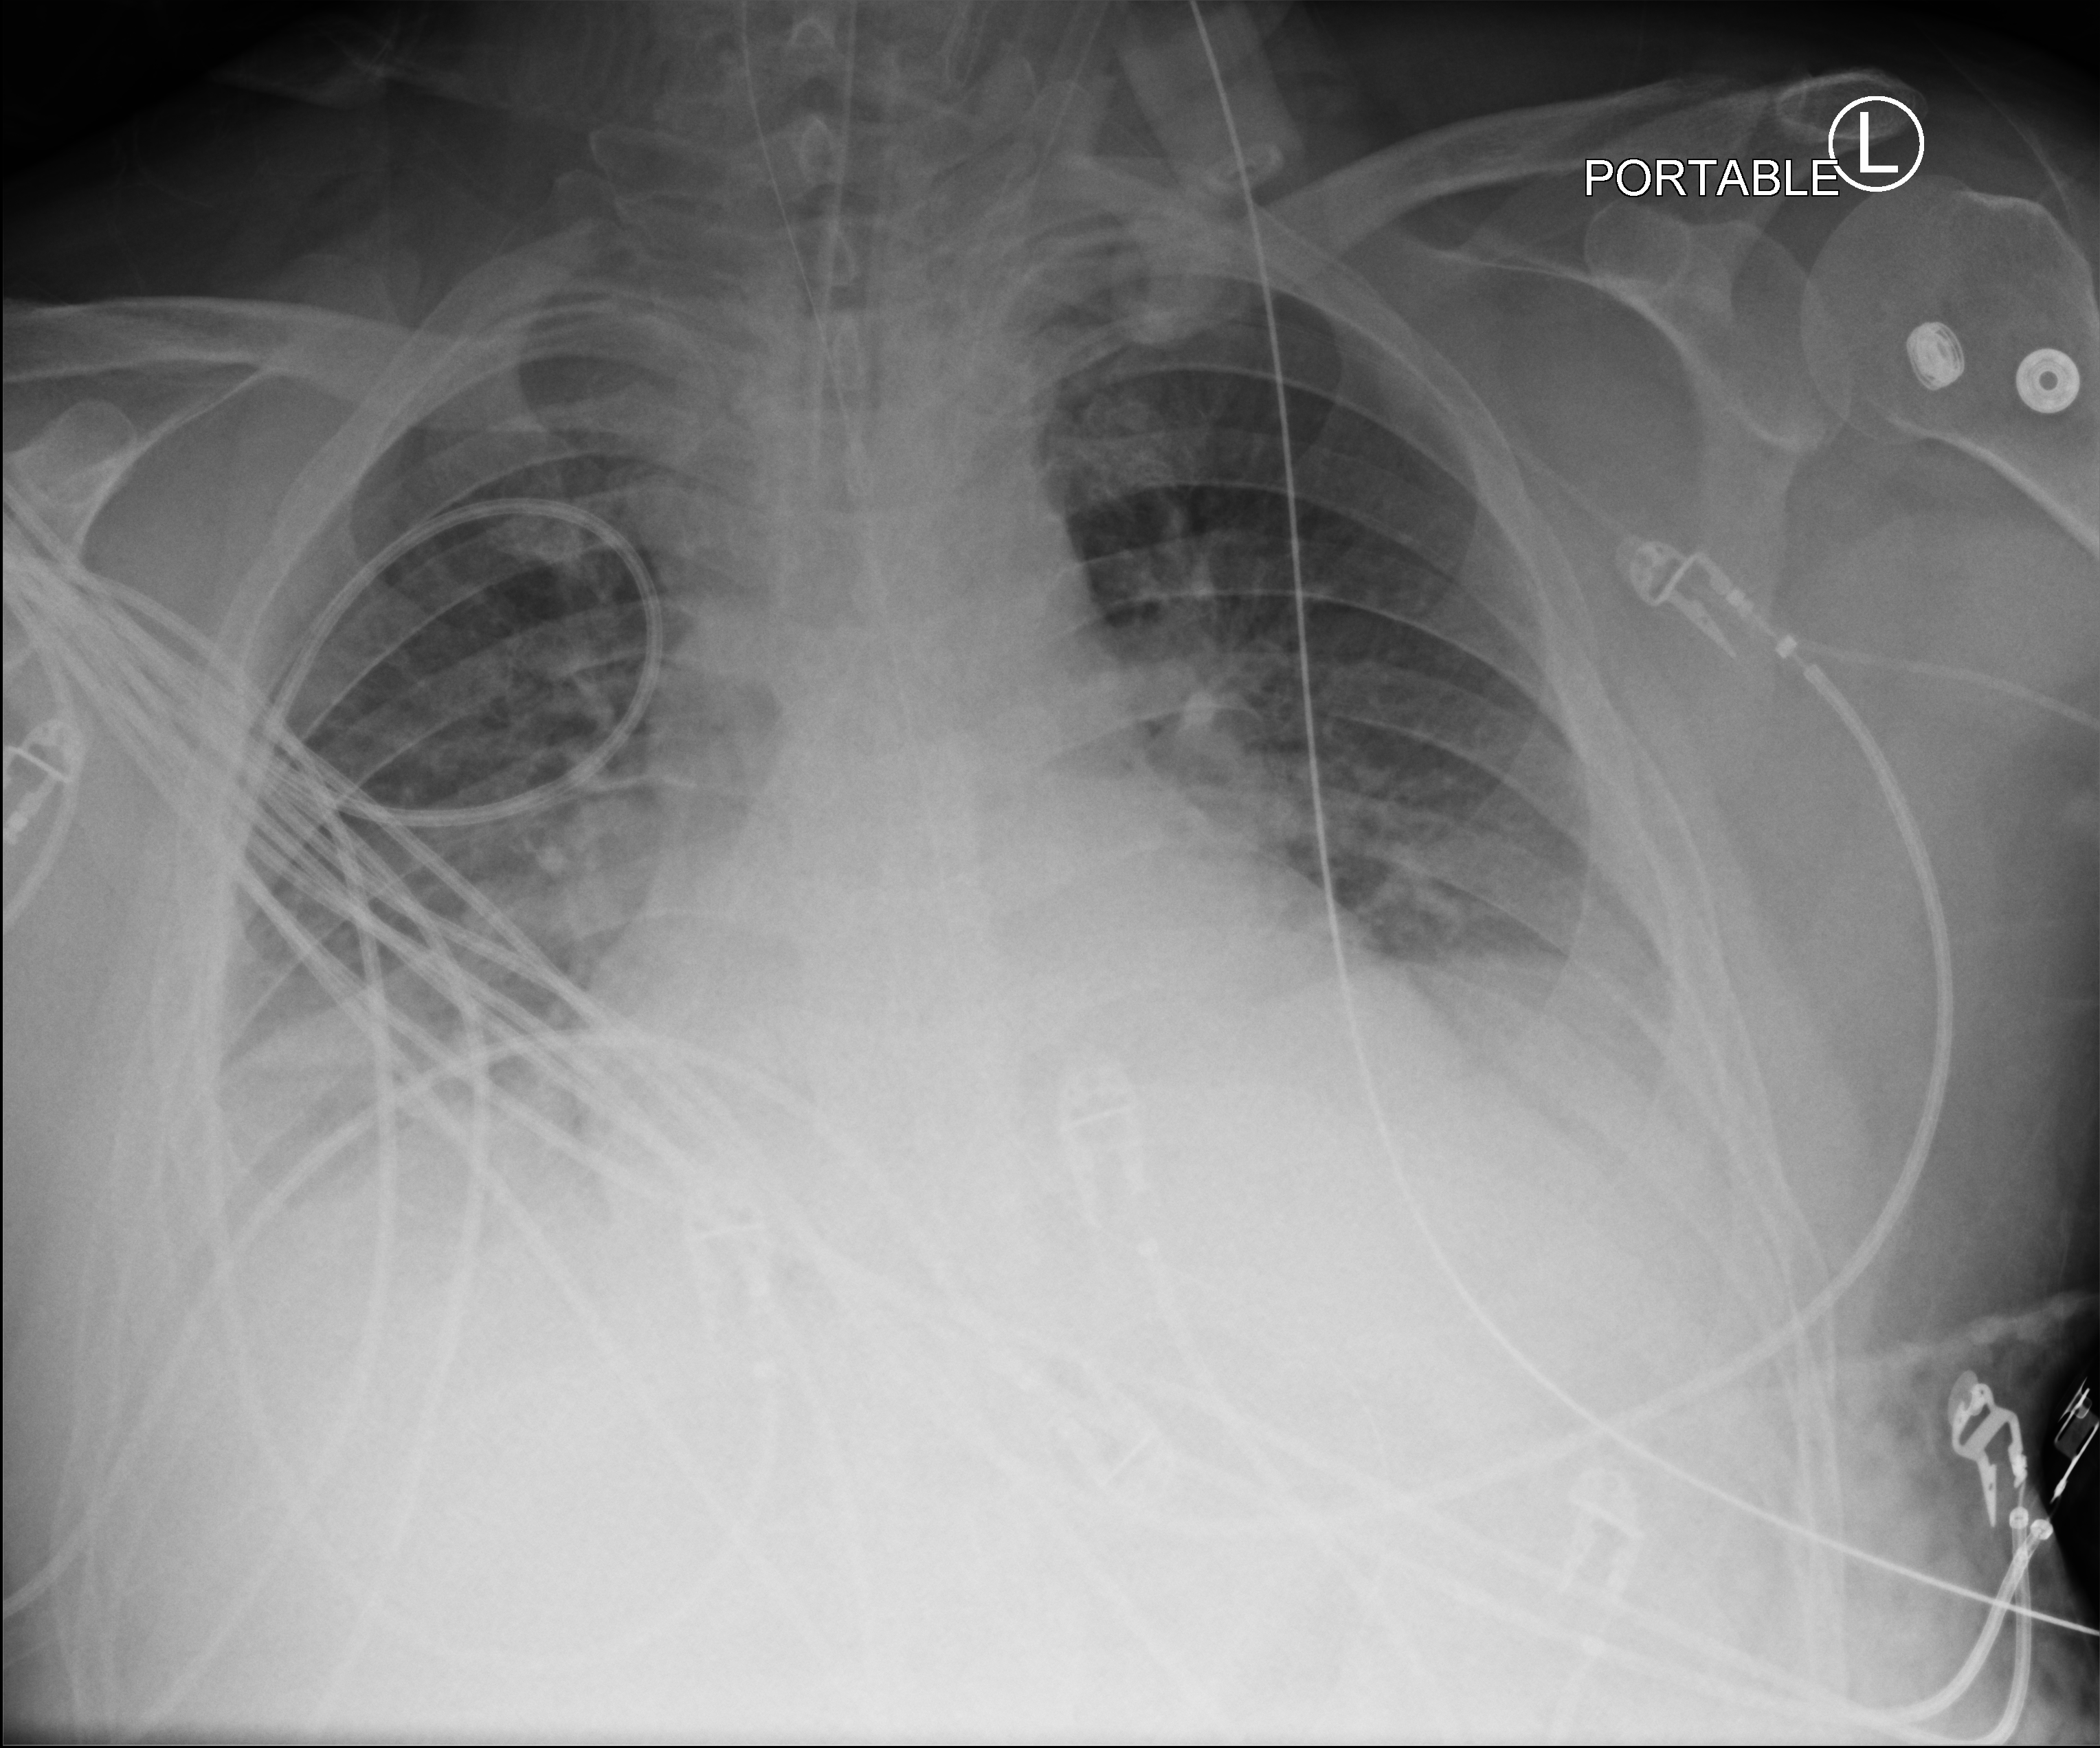
Portable chest radiograph, anteroposterior (AP) projection. Patient hospitalised with COVID-19; male, aged 18–59 years.
Hospital-stay facts (about this admission, not read from this image; timing relative to this image not recorded):
- length of hospital stay: 65 days
- mechanically ventilated during this hospital stay: yes
- admitted to intensive care during this hospital stay: yes